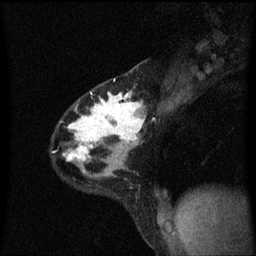
Breast MRI (dynamic contrast-enhanced), one sagittal slice. Slice 41 of 60 in the series (ordered by position). Dynamic contrast-enhanced series, image 2 of 3 at this slice position (ordered by acquisition). 1.5 T. TE 4.2 ms, TR 8.4 ms. 2 mm slice thickness. 256 × 256 image matrix, field of view 200 × 200 mm. Patient: female, 32 years.
Annotated regions visible in this slice (semi-automatically segmented with operator editing):
- analysis volume of interest (the breast-tissue region the enhancement analysis was run in; not a lesion): bounding box <54,80,148,169> (left, top, right, bottom; pixels)
- tumour enhancement mask (voxels above the 70 % enhancement threshold inside the analysis volume of interest): <64,92,145,161>